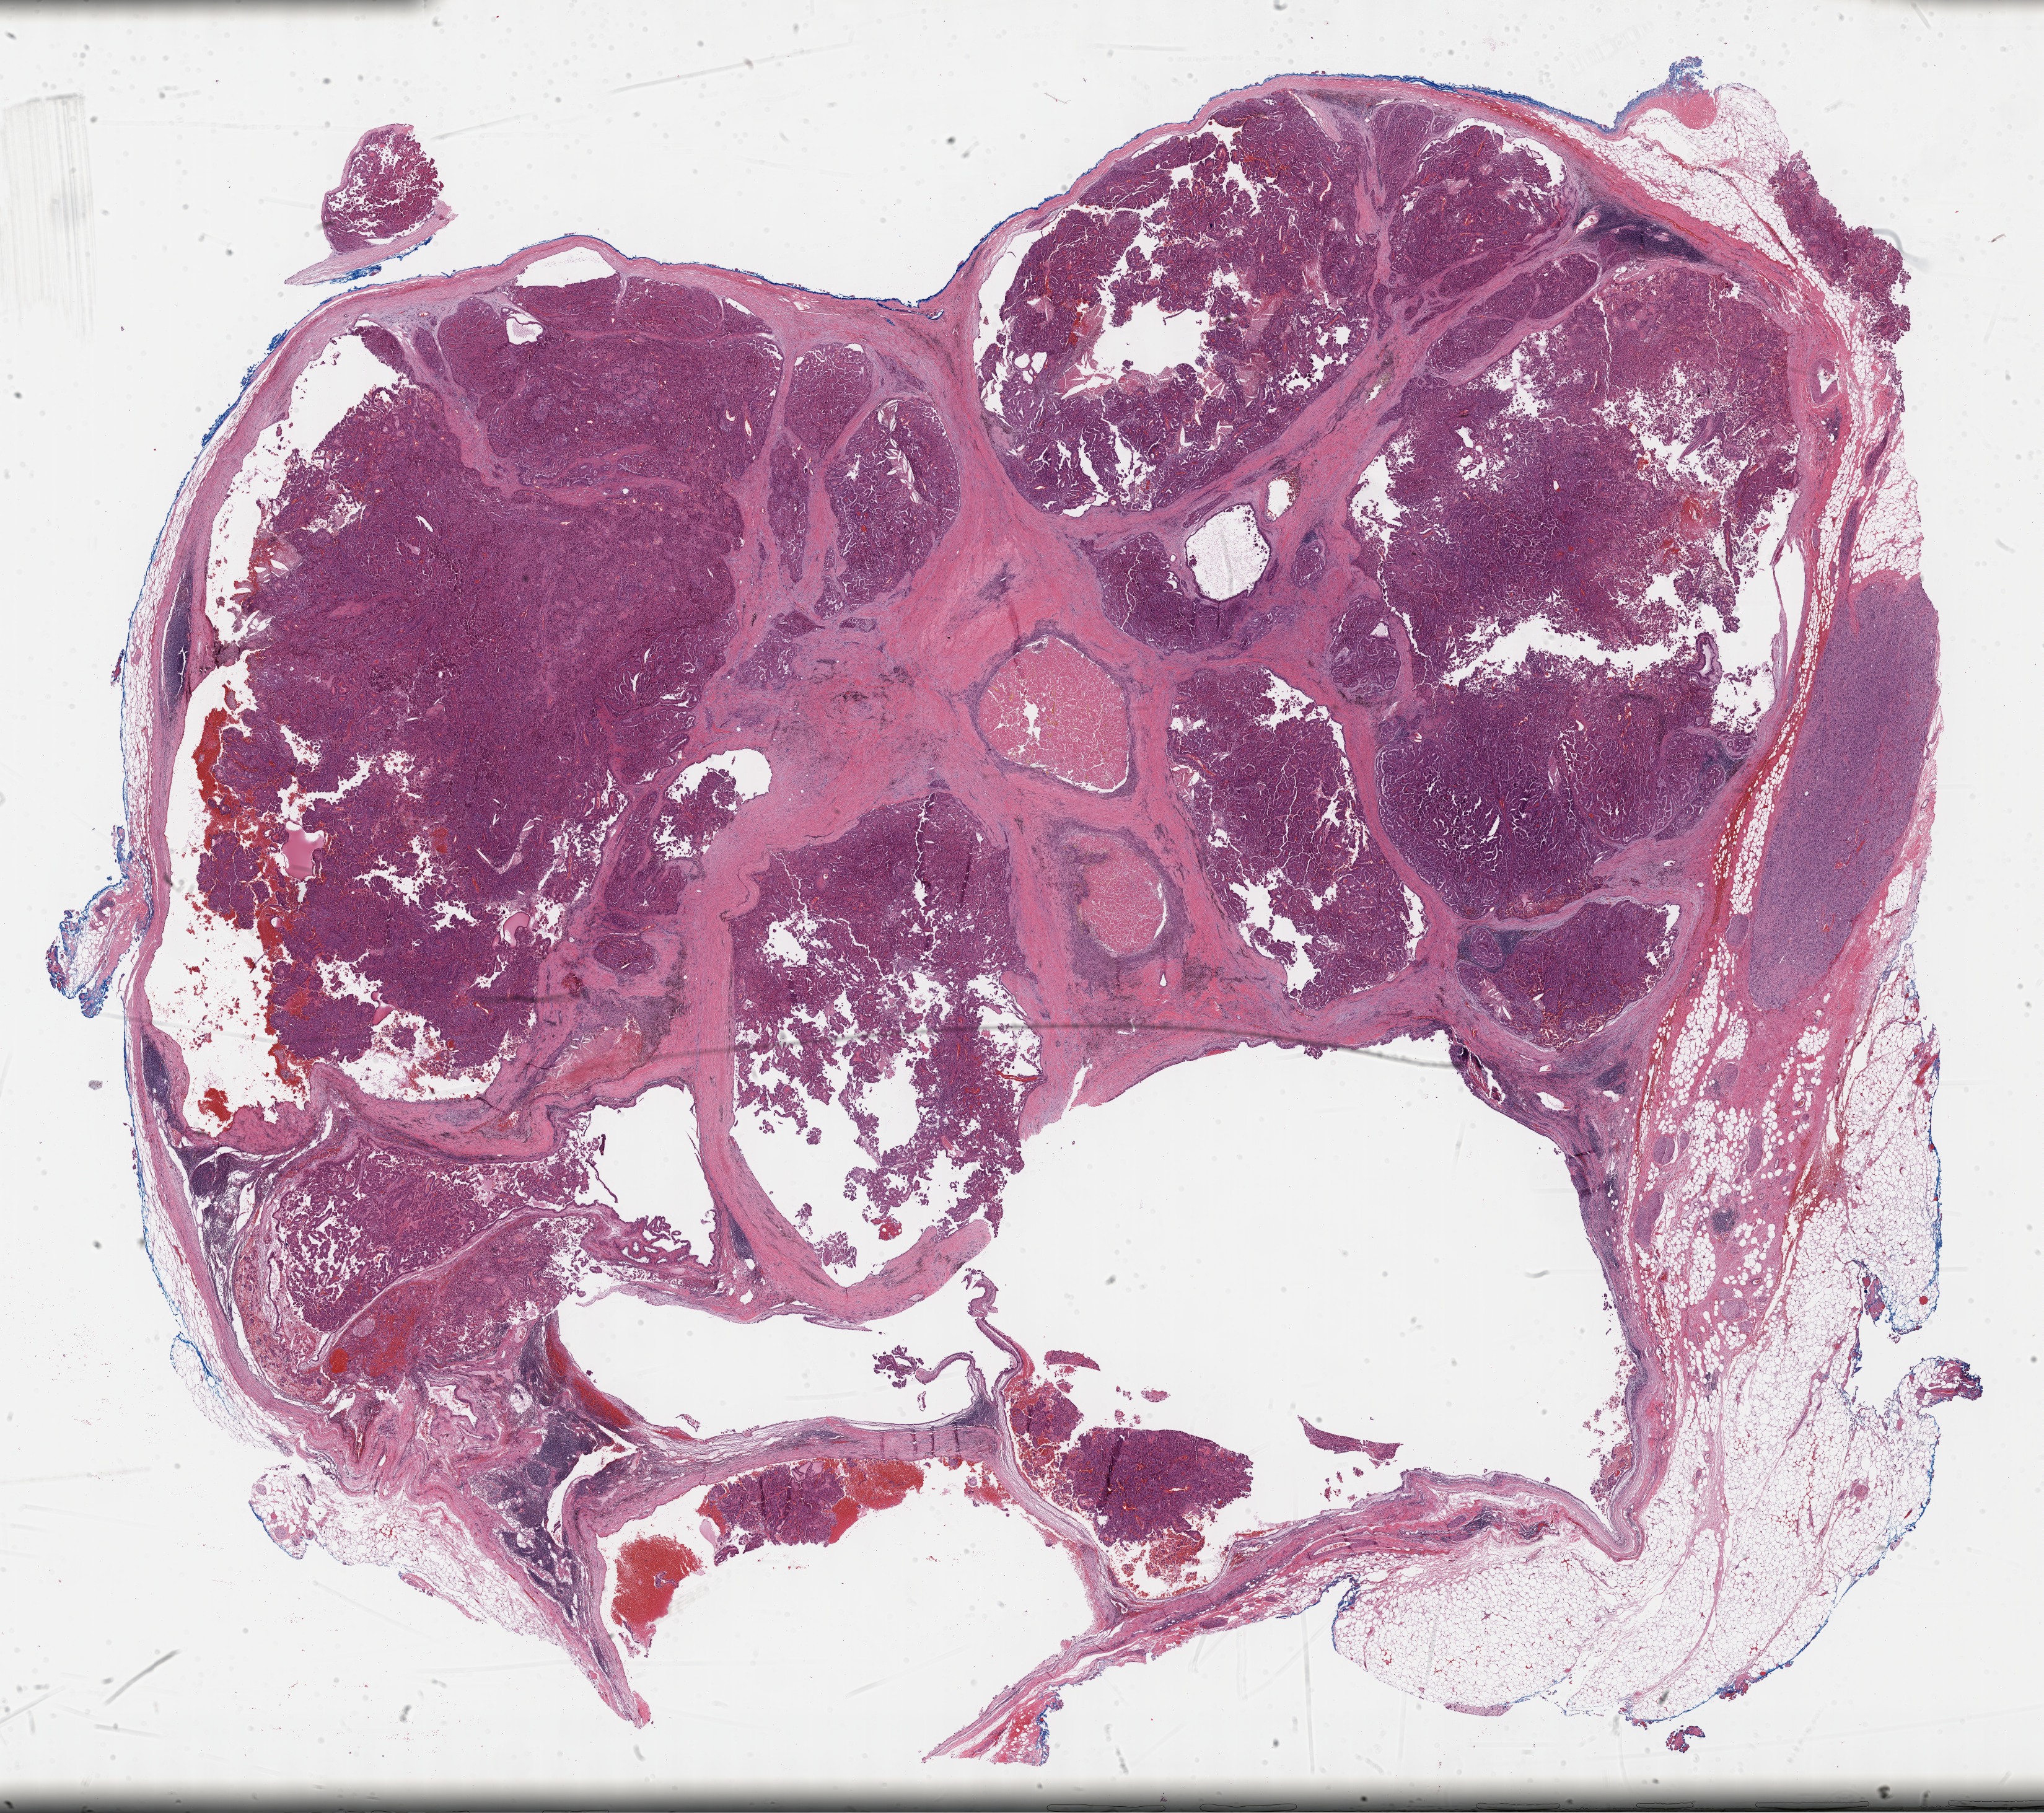
H&E whole-slide image, a low-resolution overview of the entire scanned area, about 26.7 x 23.7 mm (from a 40x scan). Formalin-fixed paraffin-embedded (FFPE) diagnostic section. Kidney, primary tumour sample. Male, age 58 years at initial diagnosis.
AJCC pathologic stage: IV (7th edition). TNM: T3a N1 MX. Histologic diagnosis: Papillary adenocarcinoma, NOS.